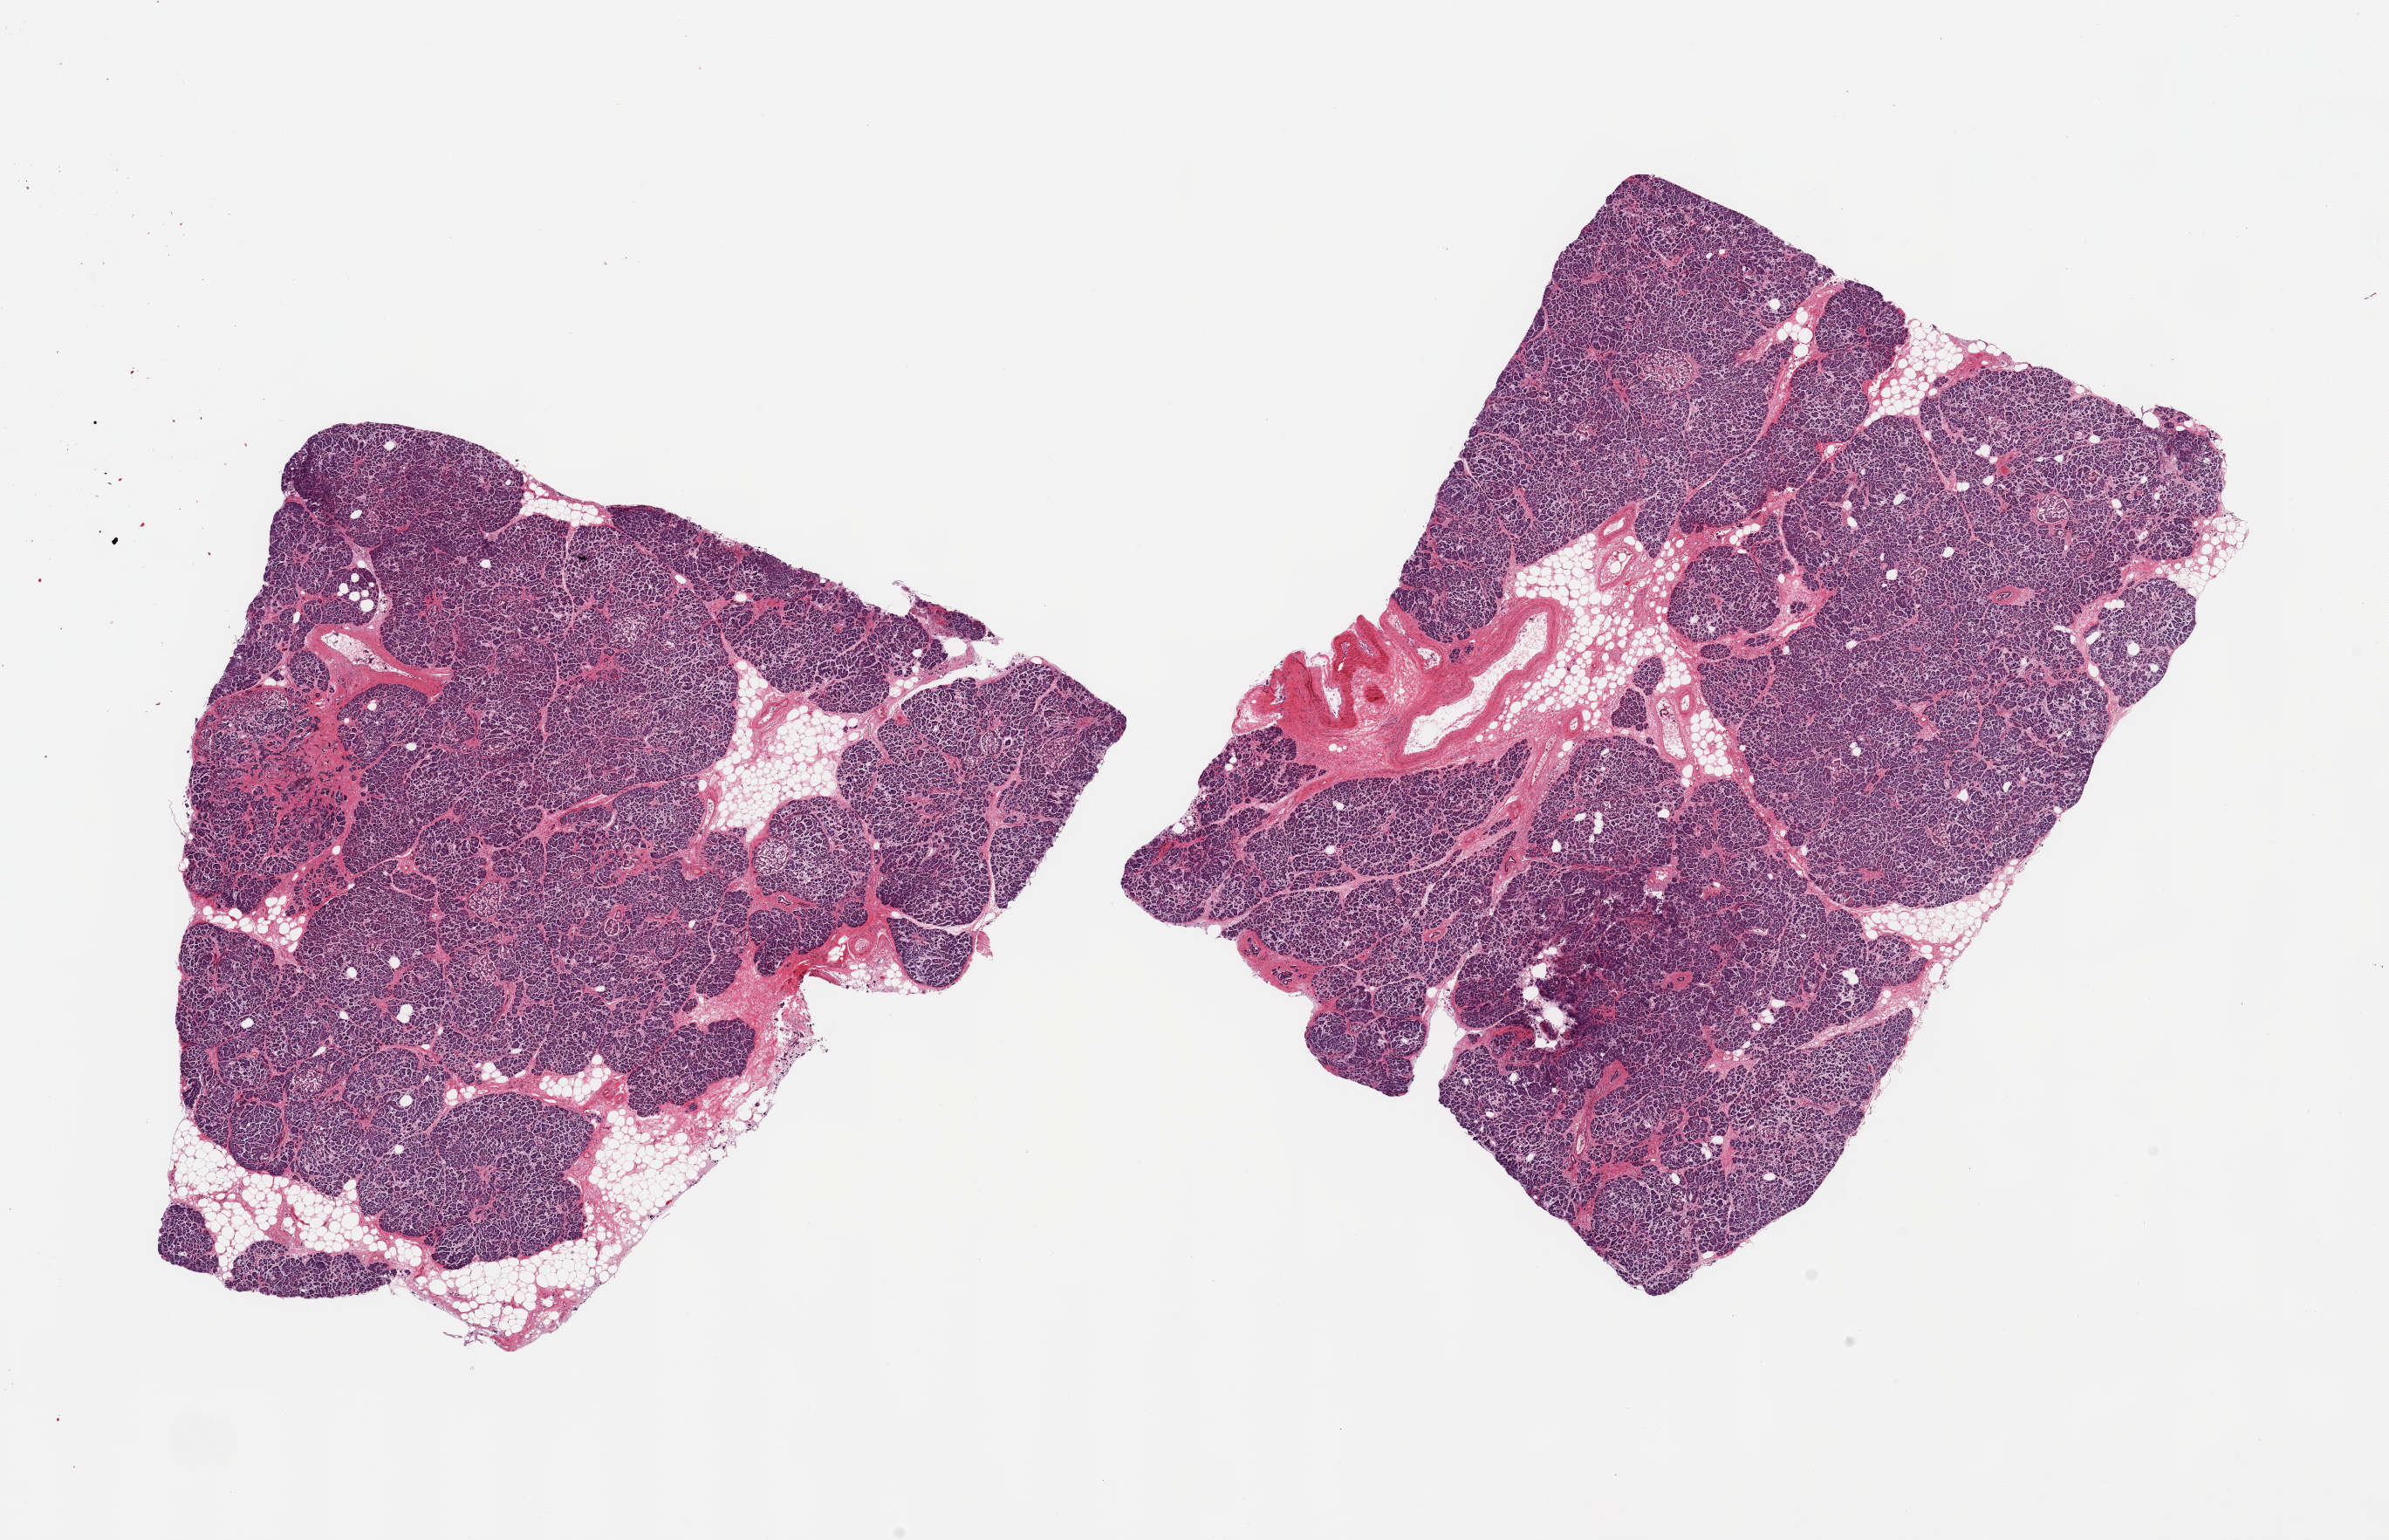
Hematoxylin and eosin (H&E) whole-slide image, a low-resolution overview of the entire scanned area, about 21.7 x 14.0 mm, PAXgene-fixed, paraffin-embedded tissue, section of pancreas (target tissue), donor tissue sample. Donor sex: male.
- reviewer comment on this tissue sample: 2 pieces, Islets vislbie , moderate saponification